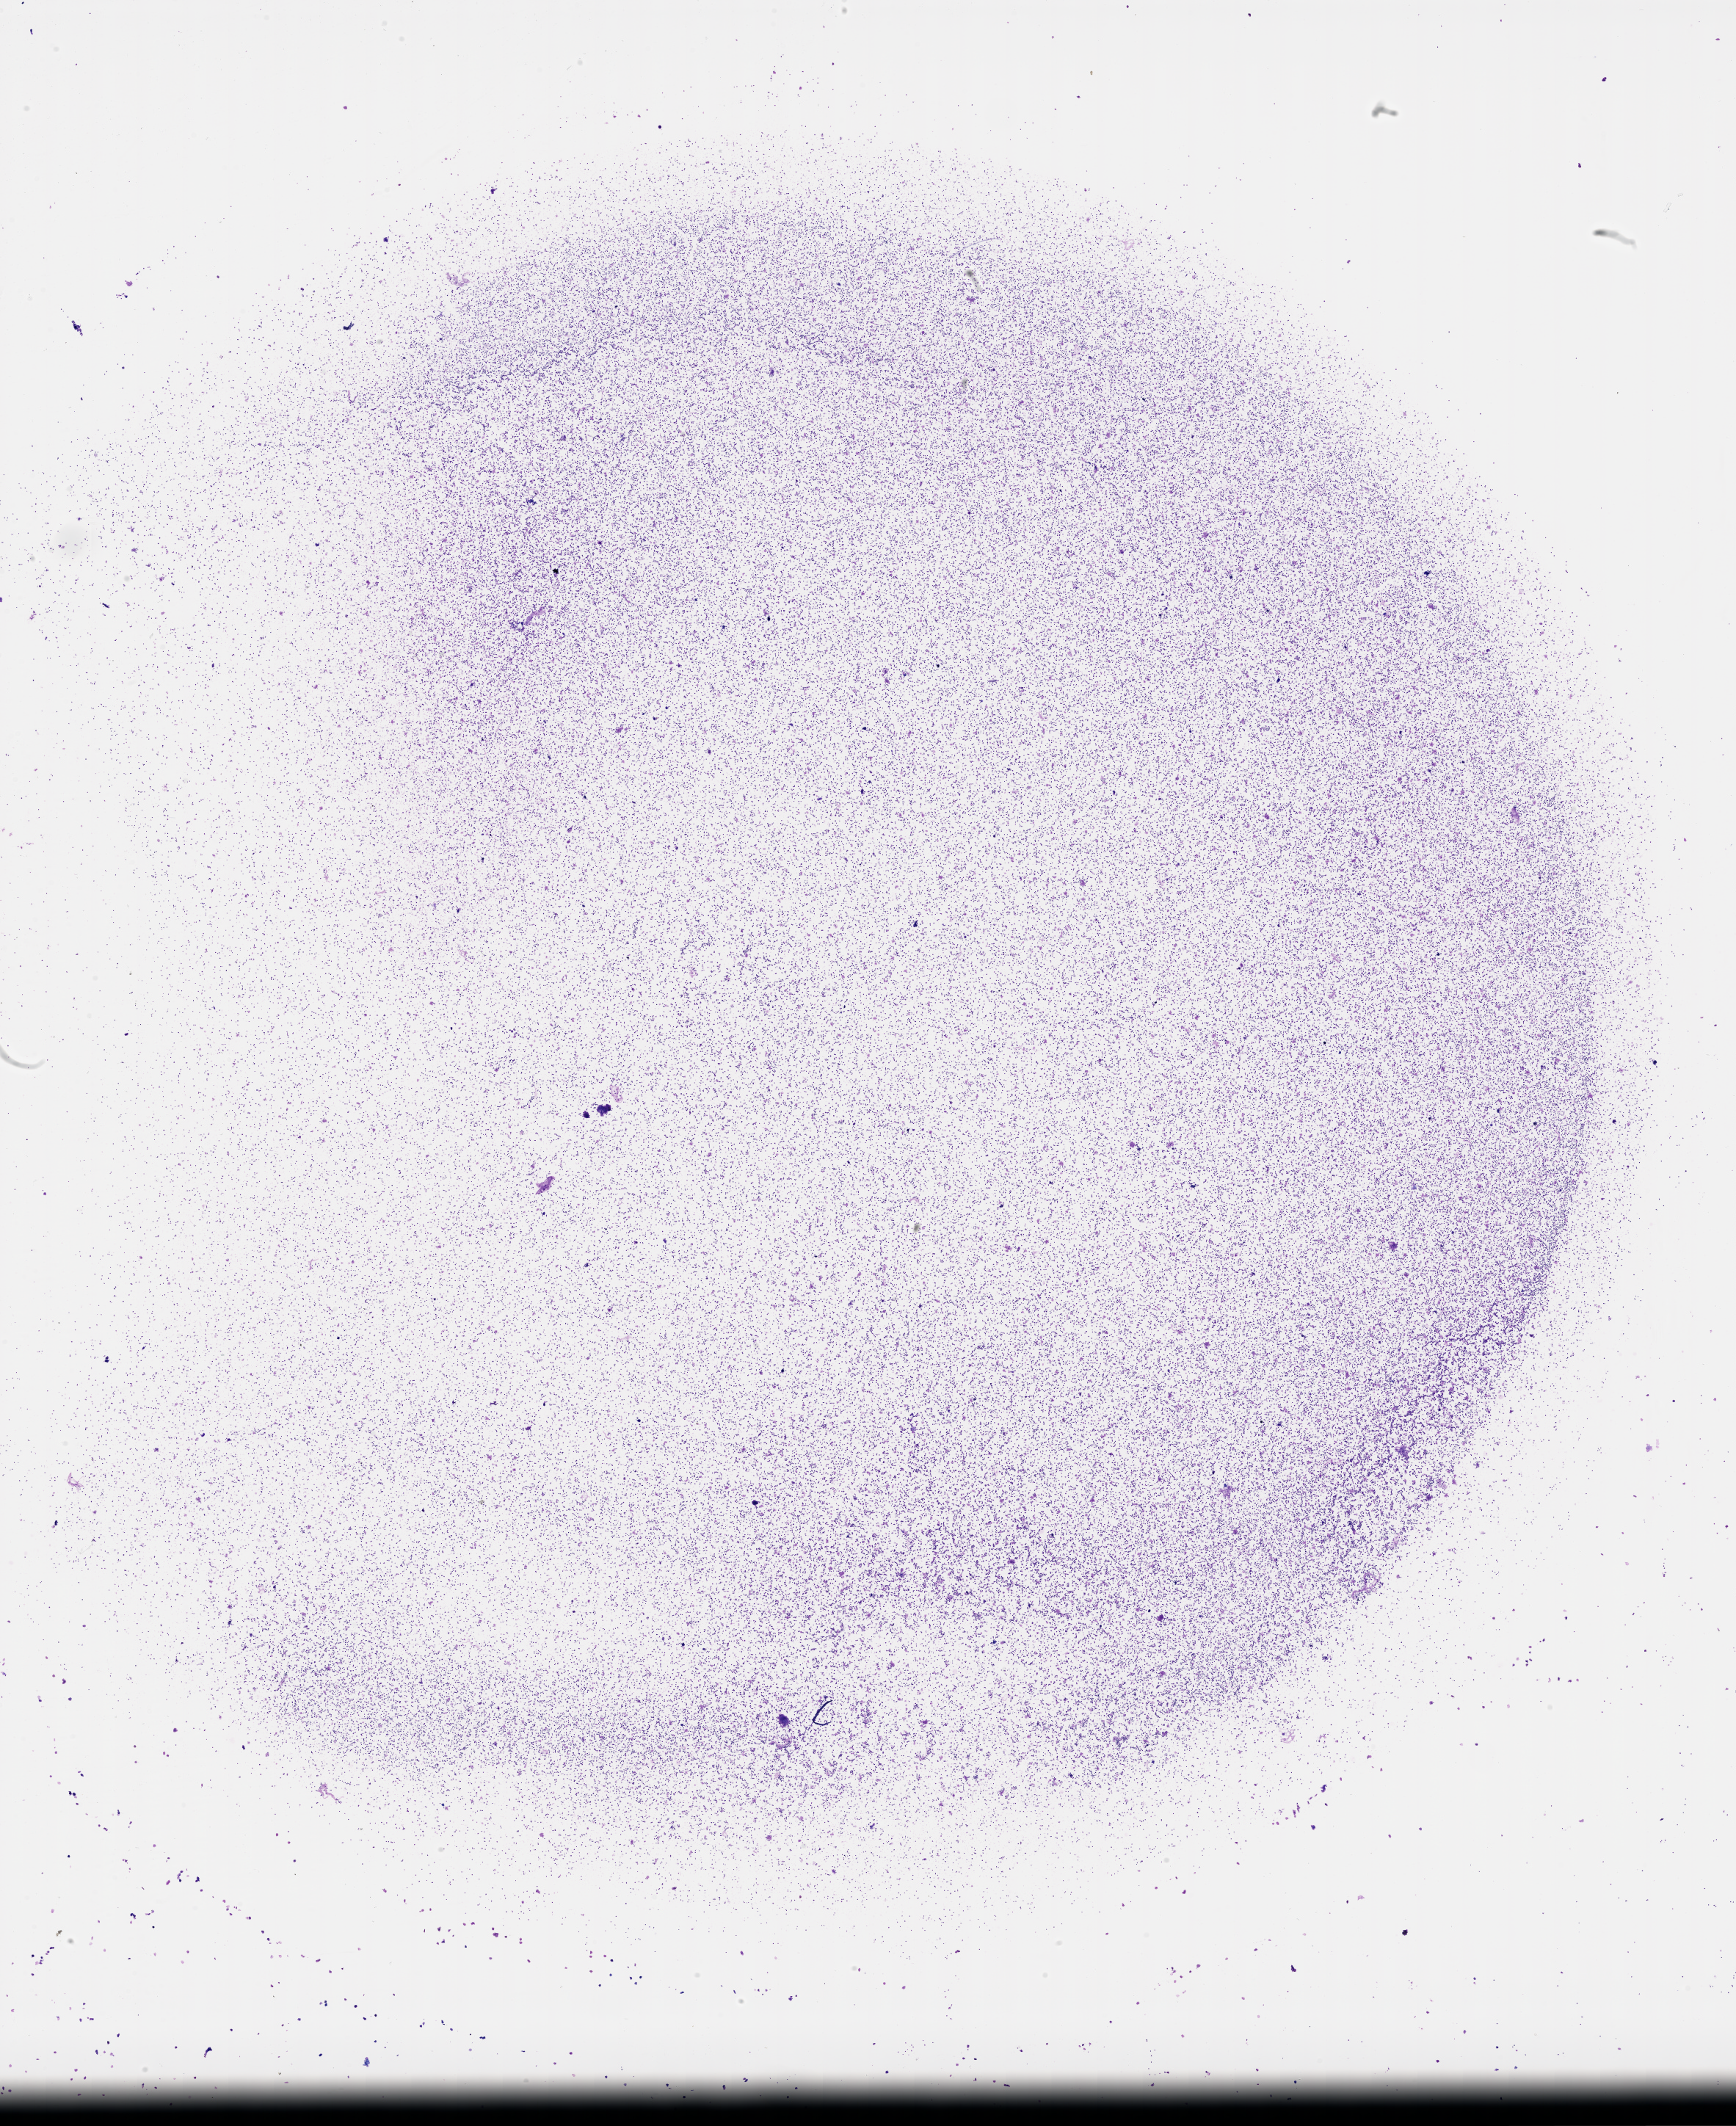
Whole-slide histology image, Hematoxylin and eosin (H&E) stained, a low-resolution overview of the entire scanned area, about 19.1 x 23.4 mm (from a 40x scan). Bone marrow (leukaemic) sample. Female, 64 y/o. Blasts: 50%.
- WHO classification: Acute megakaryoblastic leukemia
- FAB classification: M7
- diagnosis: Acute Myeloid Leukemia